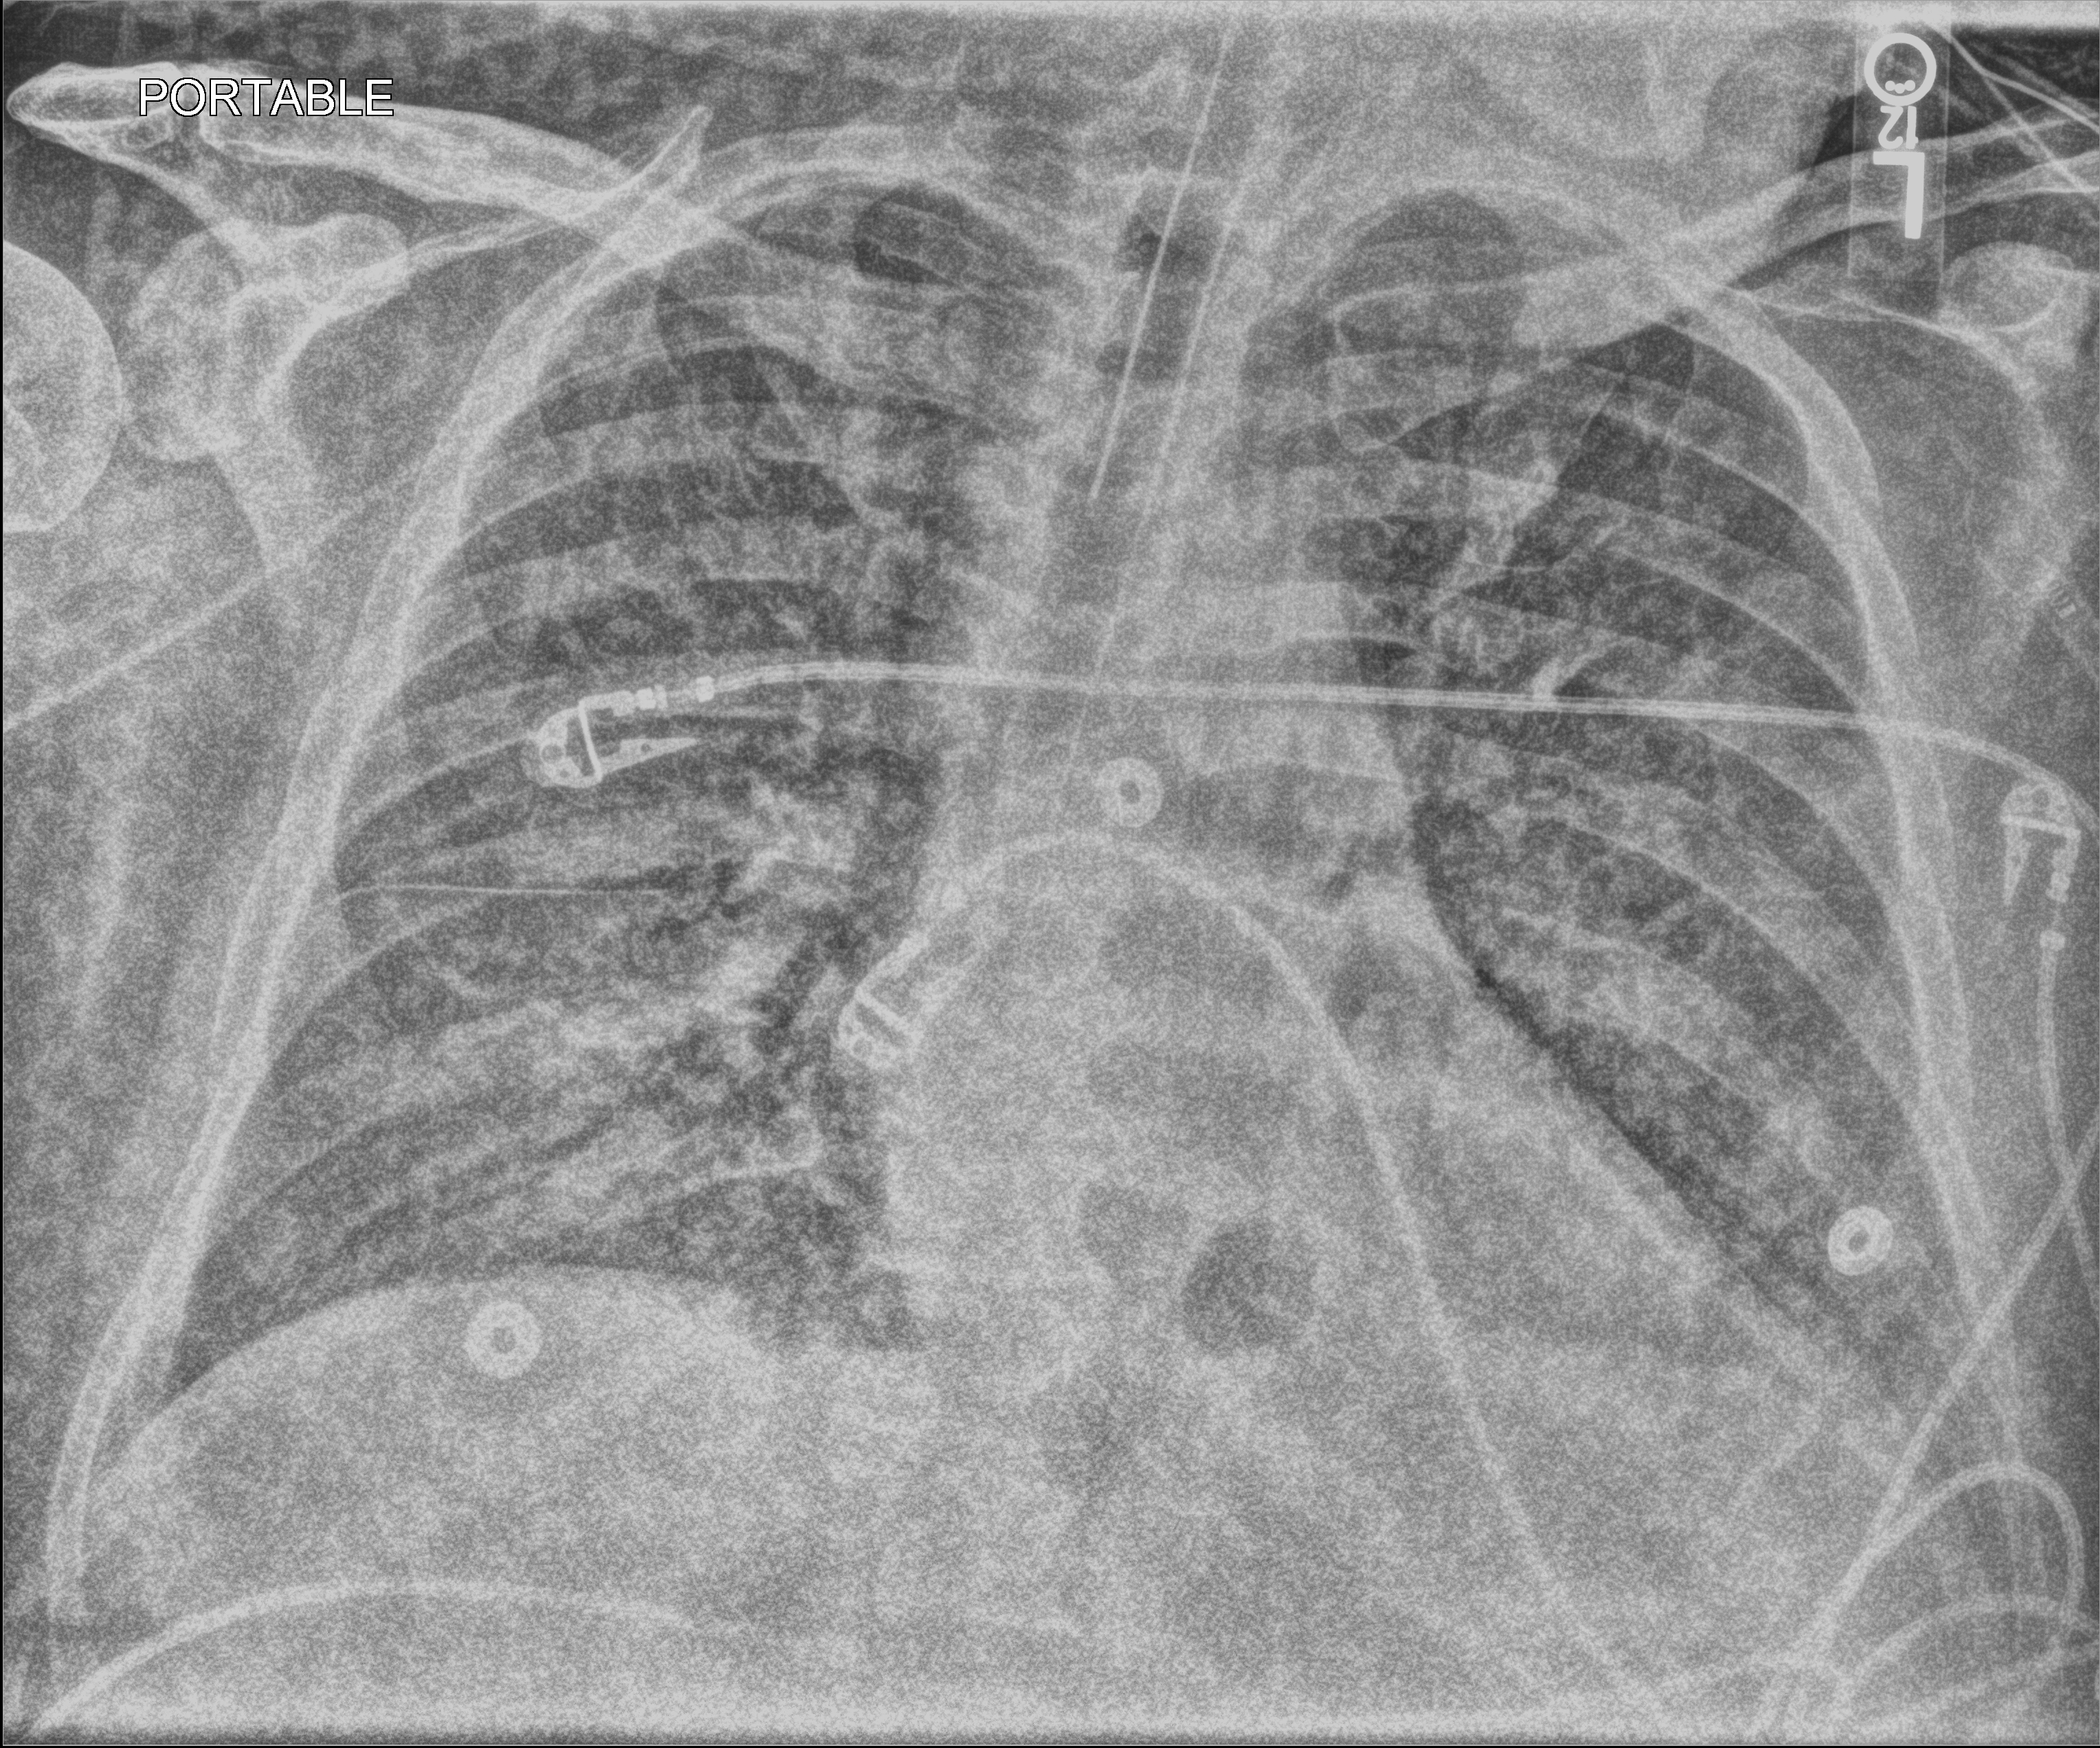
Chest X-ray (portable); anteroposterior (AP) projection. Adult patient hospitalised with COVID-19, age 18–59 years.
From the hospital-stay record, not from the radiograph (when in the stay this image was taken is not recorded): admitted to intensive care during this hospital stay: yes; length of hospital stay: 26 days.